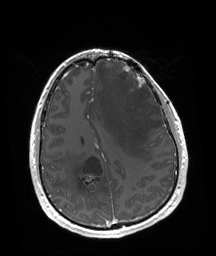
Brain MRI from a brain-tumour surgery series, one axial slice. Position 63 of 192 along the scan axis. T1-weighted post-contrast. 1 mm slice thickness. 216 × 256 image matrix, field of view 219 × 260 mm.
Structures marked on this image (outlined manually by an expert reader):
- tumour: bounding box <123,65,145,88> (left, top, right, bottom; pixels)